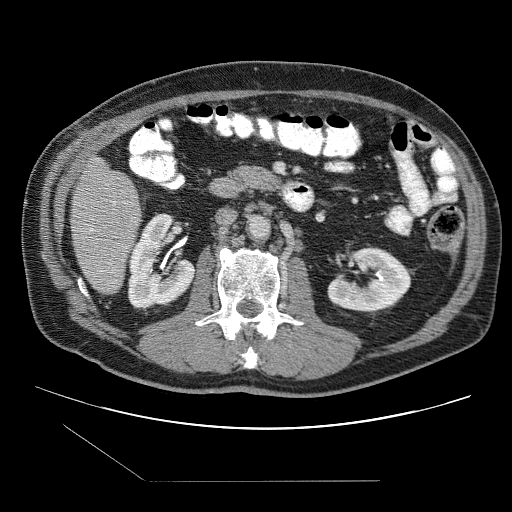
Contrast-enhanced abdominal CT (liver protocol), one axial slice. Position 27 of 109 along the scan axis. 120 kVp. One of 2 acquisitions stored at this slice position. Soft-tissue window (W 400 / L 40 HU). 2.5 mm slice thickness. 512 × 512 image matrix, field of view 400 × 400 mm. Case-level facts recorded for this patient, not image findings: diagnosis: hepatocellular carcinoma (patient treated with transarterial chemoembolisation; whether this scan precedes or follows treatment is not stated here); TNM stage (as recorded): Stage-IIIB; Child-Pugh class: A; tumour nodularity: multinodular.
Annotated regions visible in this slice (semi-automatically segmented with operator editing):
- liver parenchyma outside the tumour (the mass and vessels are separate outlines, so this box may not span the whole liver): bounding box <70,155,142,294> (left, top, right, bottom; pixels)
- liver vessels: <89,201,116,273>